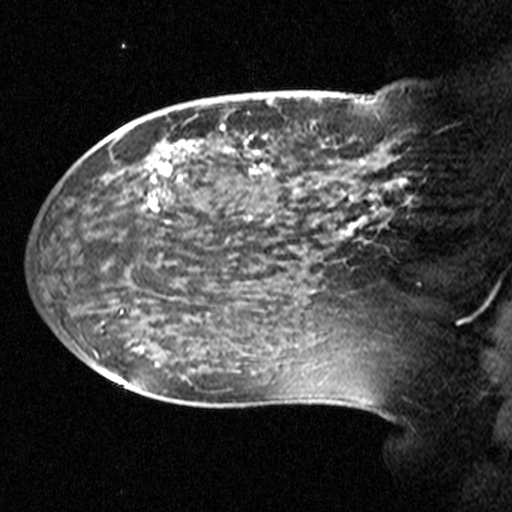
Breast MRI (dynamic contrast-enhanced), one sagittal slice; position 14 of 44 along the scan axis; dynamic contrast-enhanced study with each time point stored as its own series, time point 2 of 3 at this slice position (early post-contrast, ordered by acquisition time); 1.5 T; TE 4.5 ms, TR 11 ms; 512 × 512 image matrix. Female patient, age 38 years. From the clinical record (not read from this slice): setting: breast cancer imaged before/during neoadjuvant chemotherapy; receptor status: HR-positive, HER2-negative.
Outlined on this slice (semi-automatically segmented with operator editing):
- analysis volume of interest (the breast-tissue region the enhancement analysis was run in; not a lesion): bounding box [x1, y1, x2, y2] px = [124, 106, 405, 245]
- tumour enhancement mask (voxels above the 90 % enhancement threshold inside the analysis volume of interest): [161, 142, 405, 183]